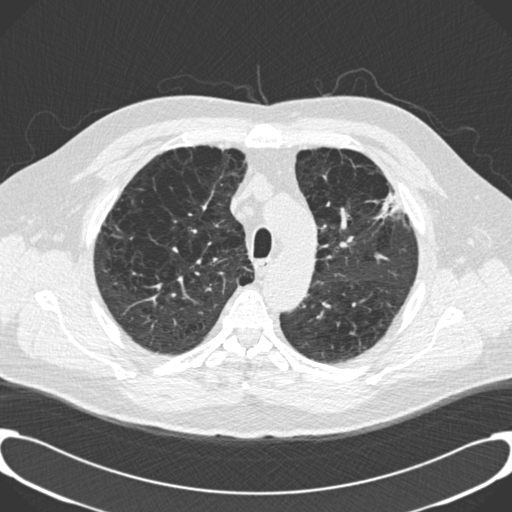
Low-dose screening chest CT, axial slice; third annual screen; lung window (W 1500 / L -600 HU); 2 mm slice thickness; 120 kVp; slice 40 of 189 in the series. Male, age 59 years at enrolment.
Expert reader's lesion annotation, bounding box [x1, y1, x2, y2] px = [361, 166, 413, 227]. Screening reader's record for this exam: no non-calcified nodule ≥4 mm recorded. Official screen result: positive, other. Lung cancer was diagnosed 134 days after this screen: bronchiolo-alveolar carcinoma, mixed mucinous and non-mucinous, left upper lobe, stage IA (AJCC 6th edition), 20 mm at pathology.